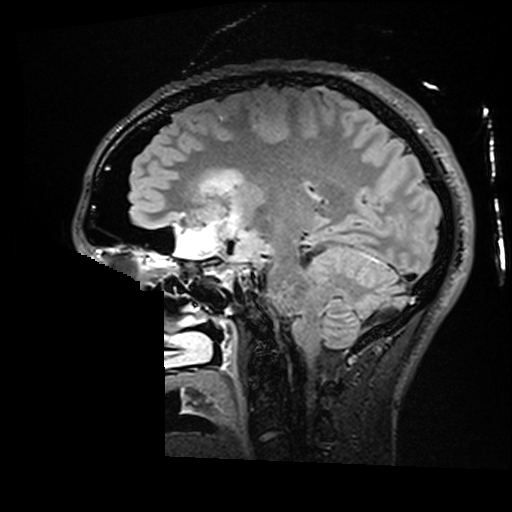
Brain MRI from a brain-tumour surgery series, one sagittal slice; position 100 of 176 along the scan axis; T2 FLAIR; 1 mm slice thickness; 512 × 512 image matrix, field of view 250 × 250 mm. Case-level facts recorded for this patient, not image findings: histopathology: Astrocytoma; WHO grade: 2; IDH mutation: yes.
Annotated regions visible in this slice (outlined manually by an expert reader):
- residual tumour: box from (x=201, y=171) to (x=243, y=194) px